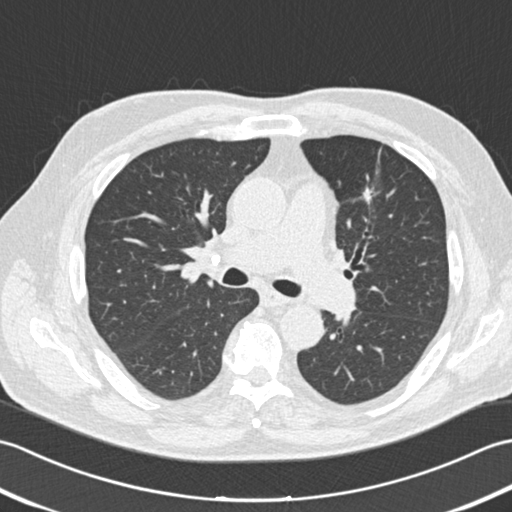
Chest CT (low-dose screening protocol), one axial image. Second annual screen. Lung window (W 1500 / L -600 HU). 2 mm slice thickness. 120 kVp. Slice 72 of 161 in the series. 512 × 512 image matrix, field of view 350 × 350 mm. Male, age 74 years at enrolment. Former smoker at enrolment.
Expert reader's lesion annotation, bounding box [x1, y1, x2, y2] px = [347, 176, 391, 214]. The screening reader recorded 5 non-calcified nodules or masses ≥4 mm on this exam (left upper lobe, right upper lobe, left lower lobe, left lower lobe, left lower lobe); which of them this box marks is not recorded. Participant outcome: lung cancer diagnosed 686 days after this screen — adenocarcinoma, NOS, left upper lobe, poorly differentiated (G3), stage IIIA (AJCC 6th edition), 27 mm at pathology.